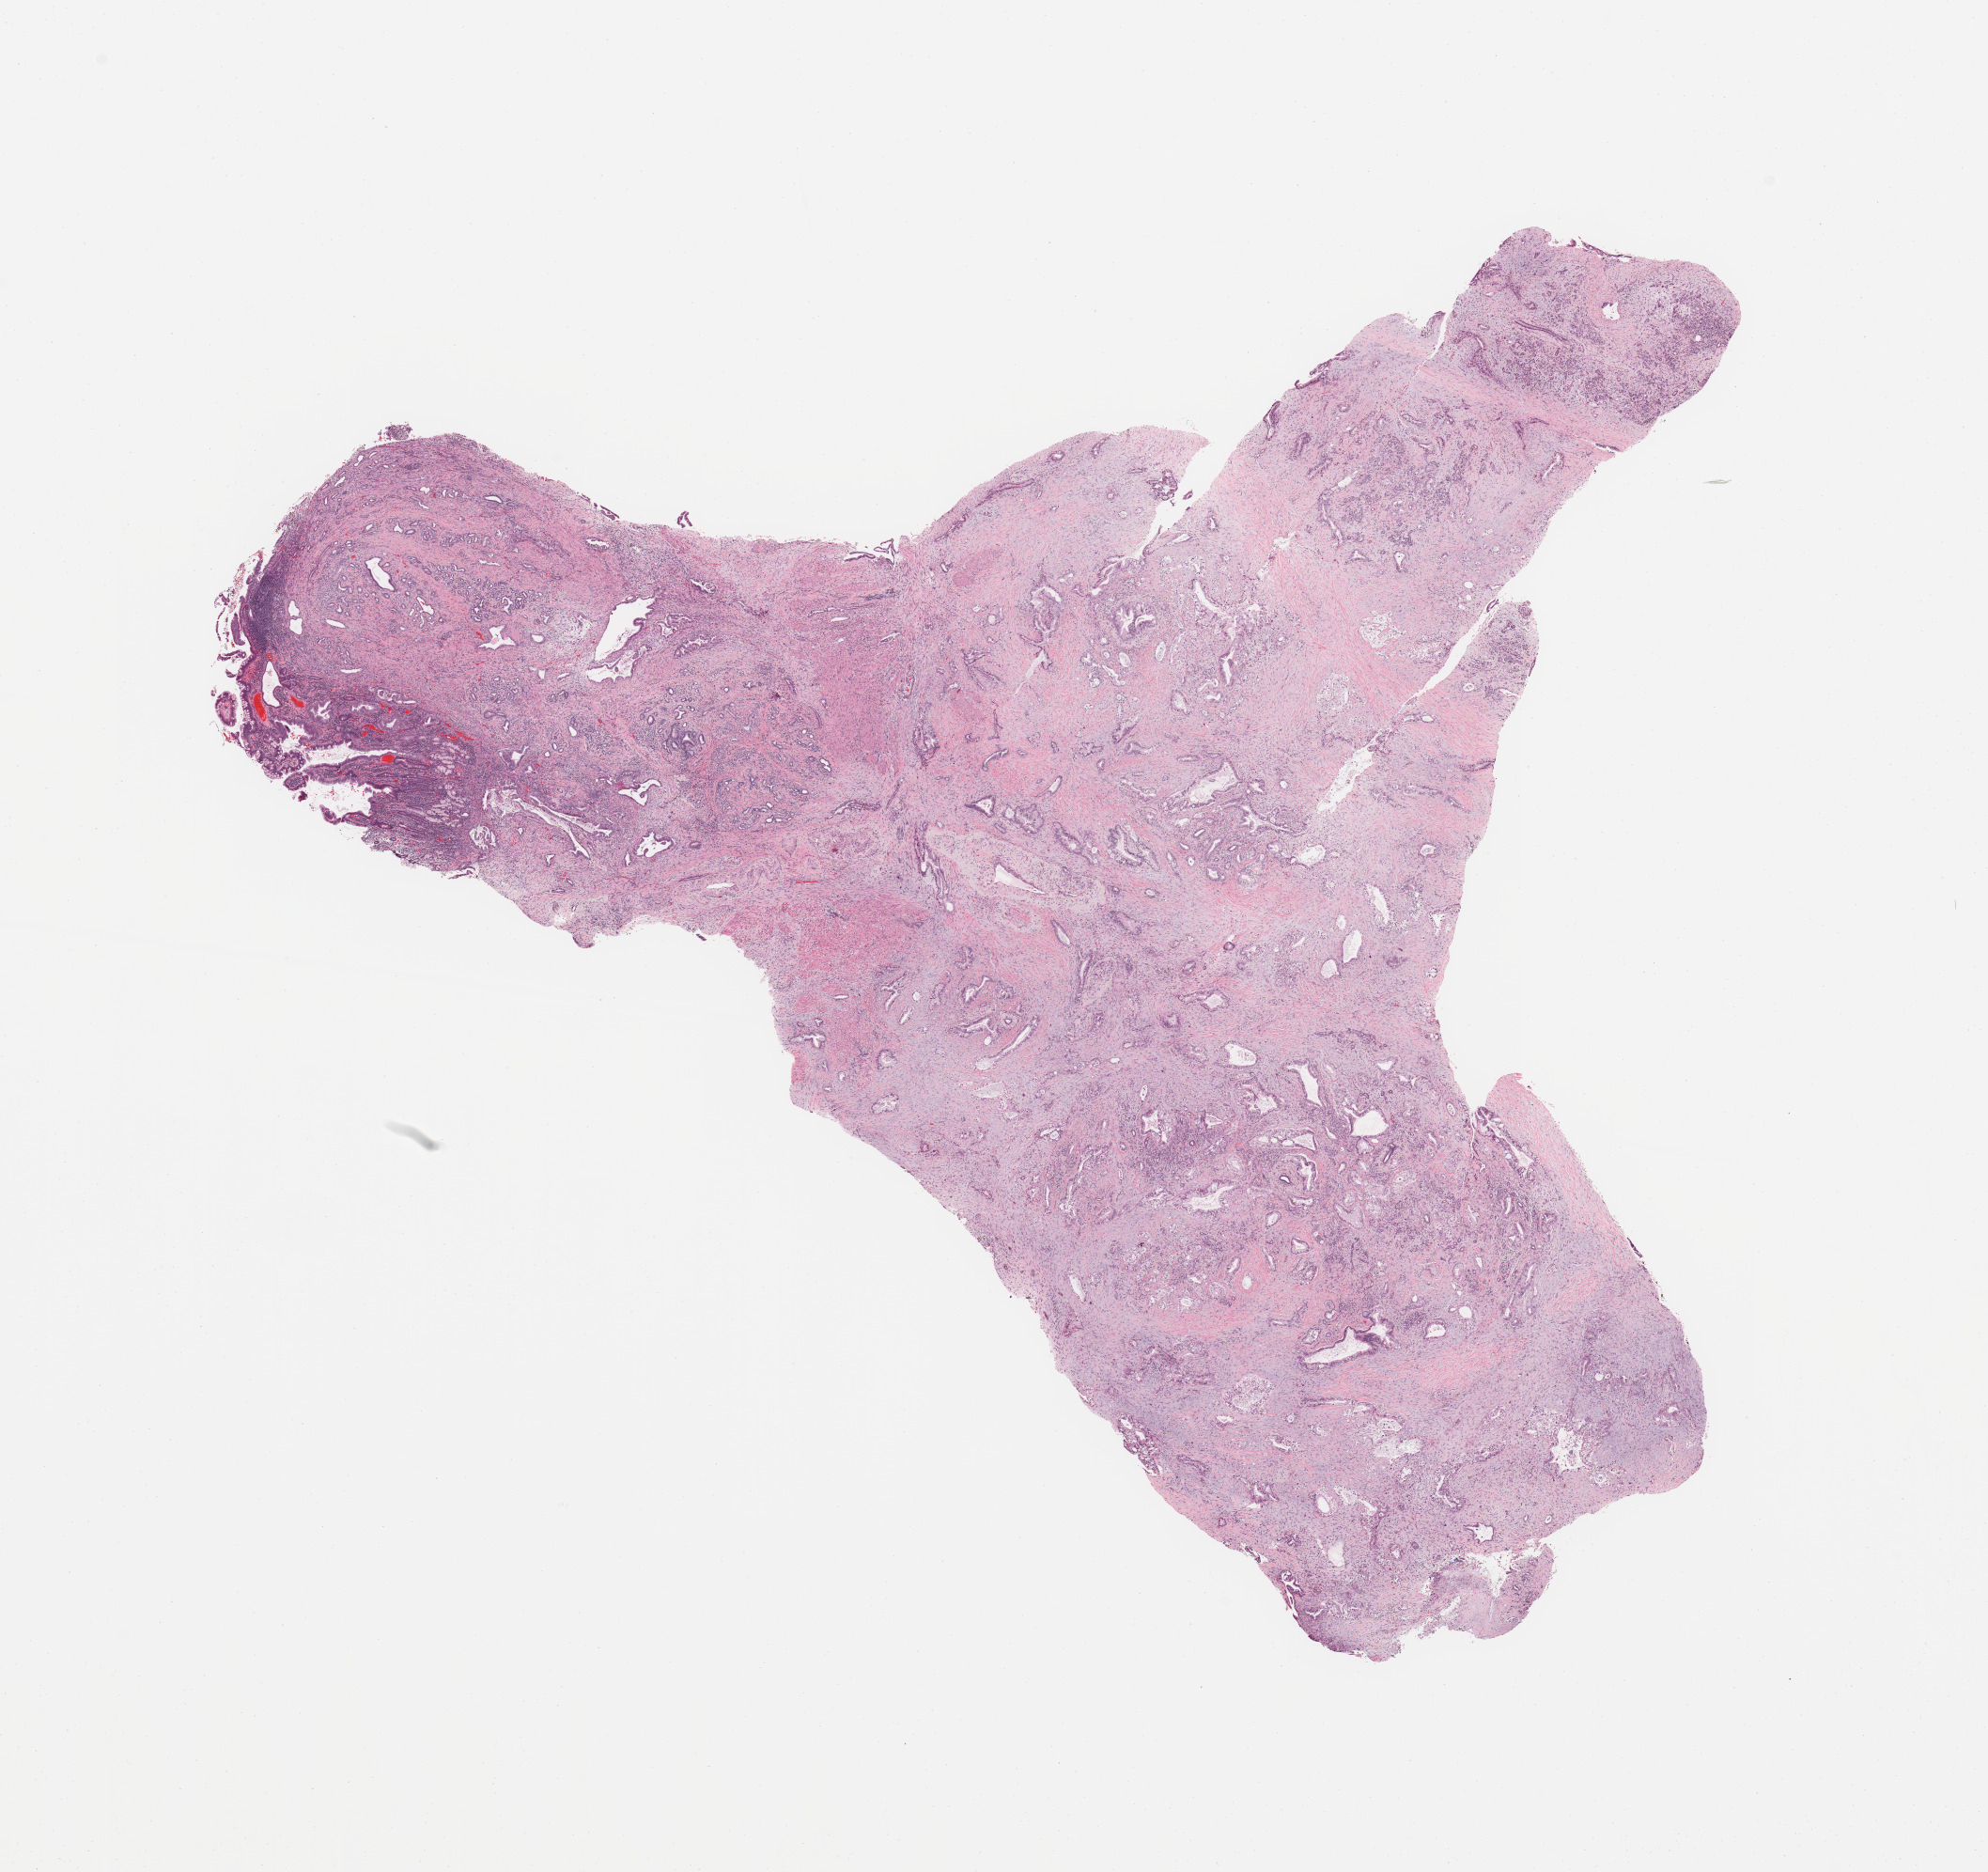
Hematoxylin and eosin (H&E) stained whole-slide image, a low-resolution overview of the entire scanned area, about 16.7 x 15.8 mm (from a 20x scan). Pancreas, tumour tissue. 73-year-old male patient.
Histologic diagnosis: Infiltrating duct carcinoma, NOS.